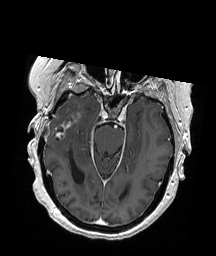
Brain MRI from a brain-tumour surgery series, one axial slice. T1-weighted post-contrast. 1 mm slice thickness. 216 × 256 image matrix, field of view 211 × 250 mm. From the clinical record (not read from this slice): histopathology: Glioblastoma; WHO grade: 4; IDH mutation: no; tumour location: Right Temporal.
Outlined on this slice (manually delineated by an expert):
- tumour: bounding box (x1, y1, x2, y2) in pixels: (54, 114, 80, 139)